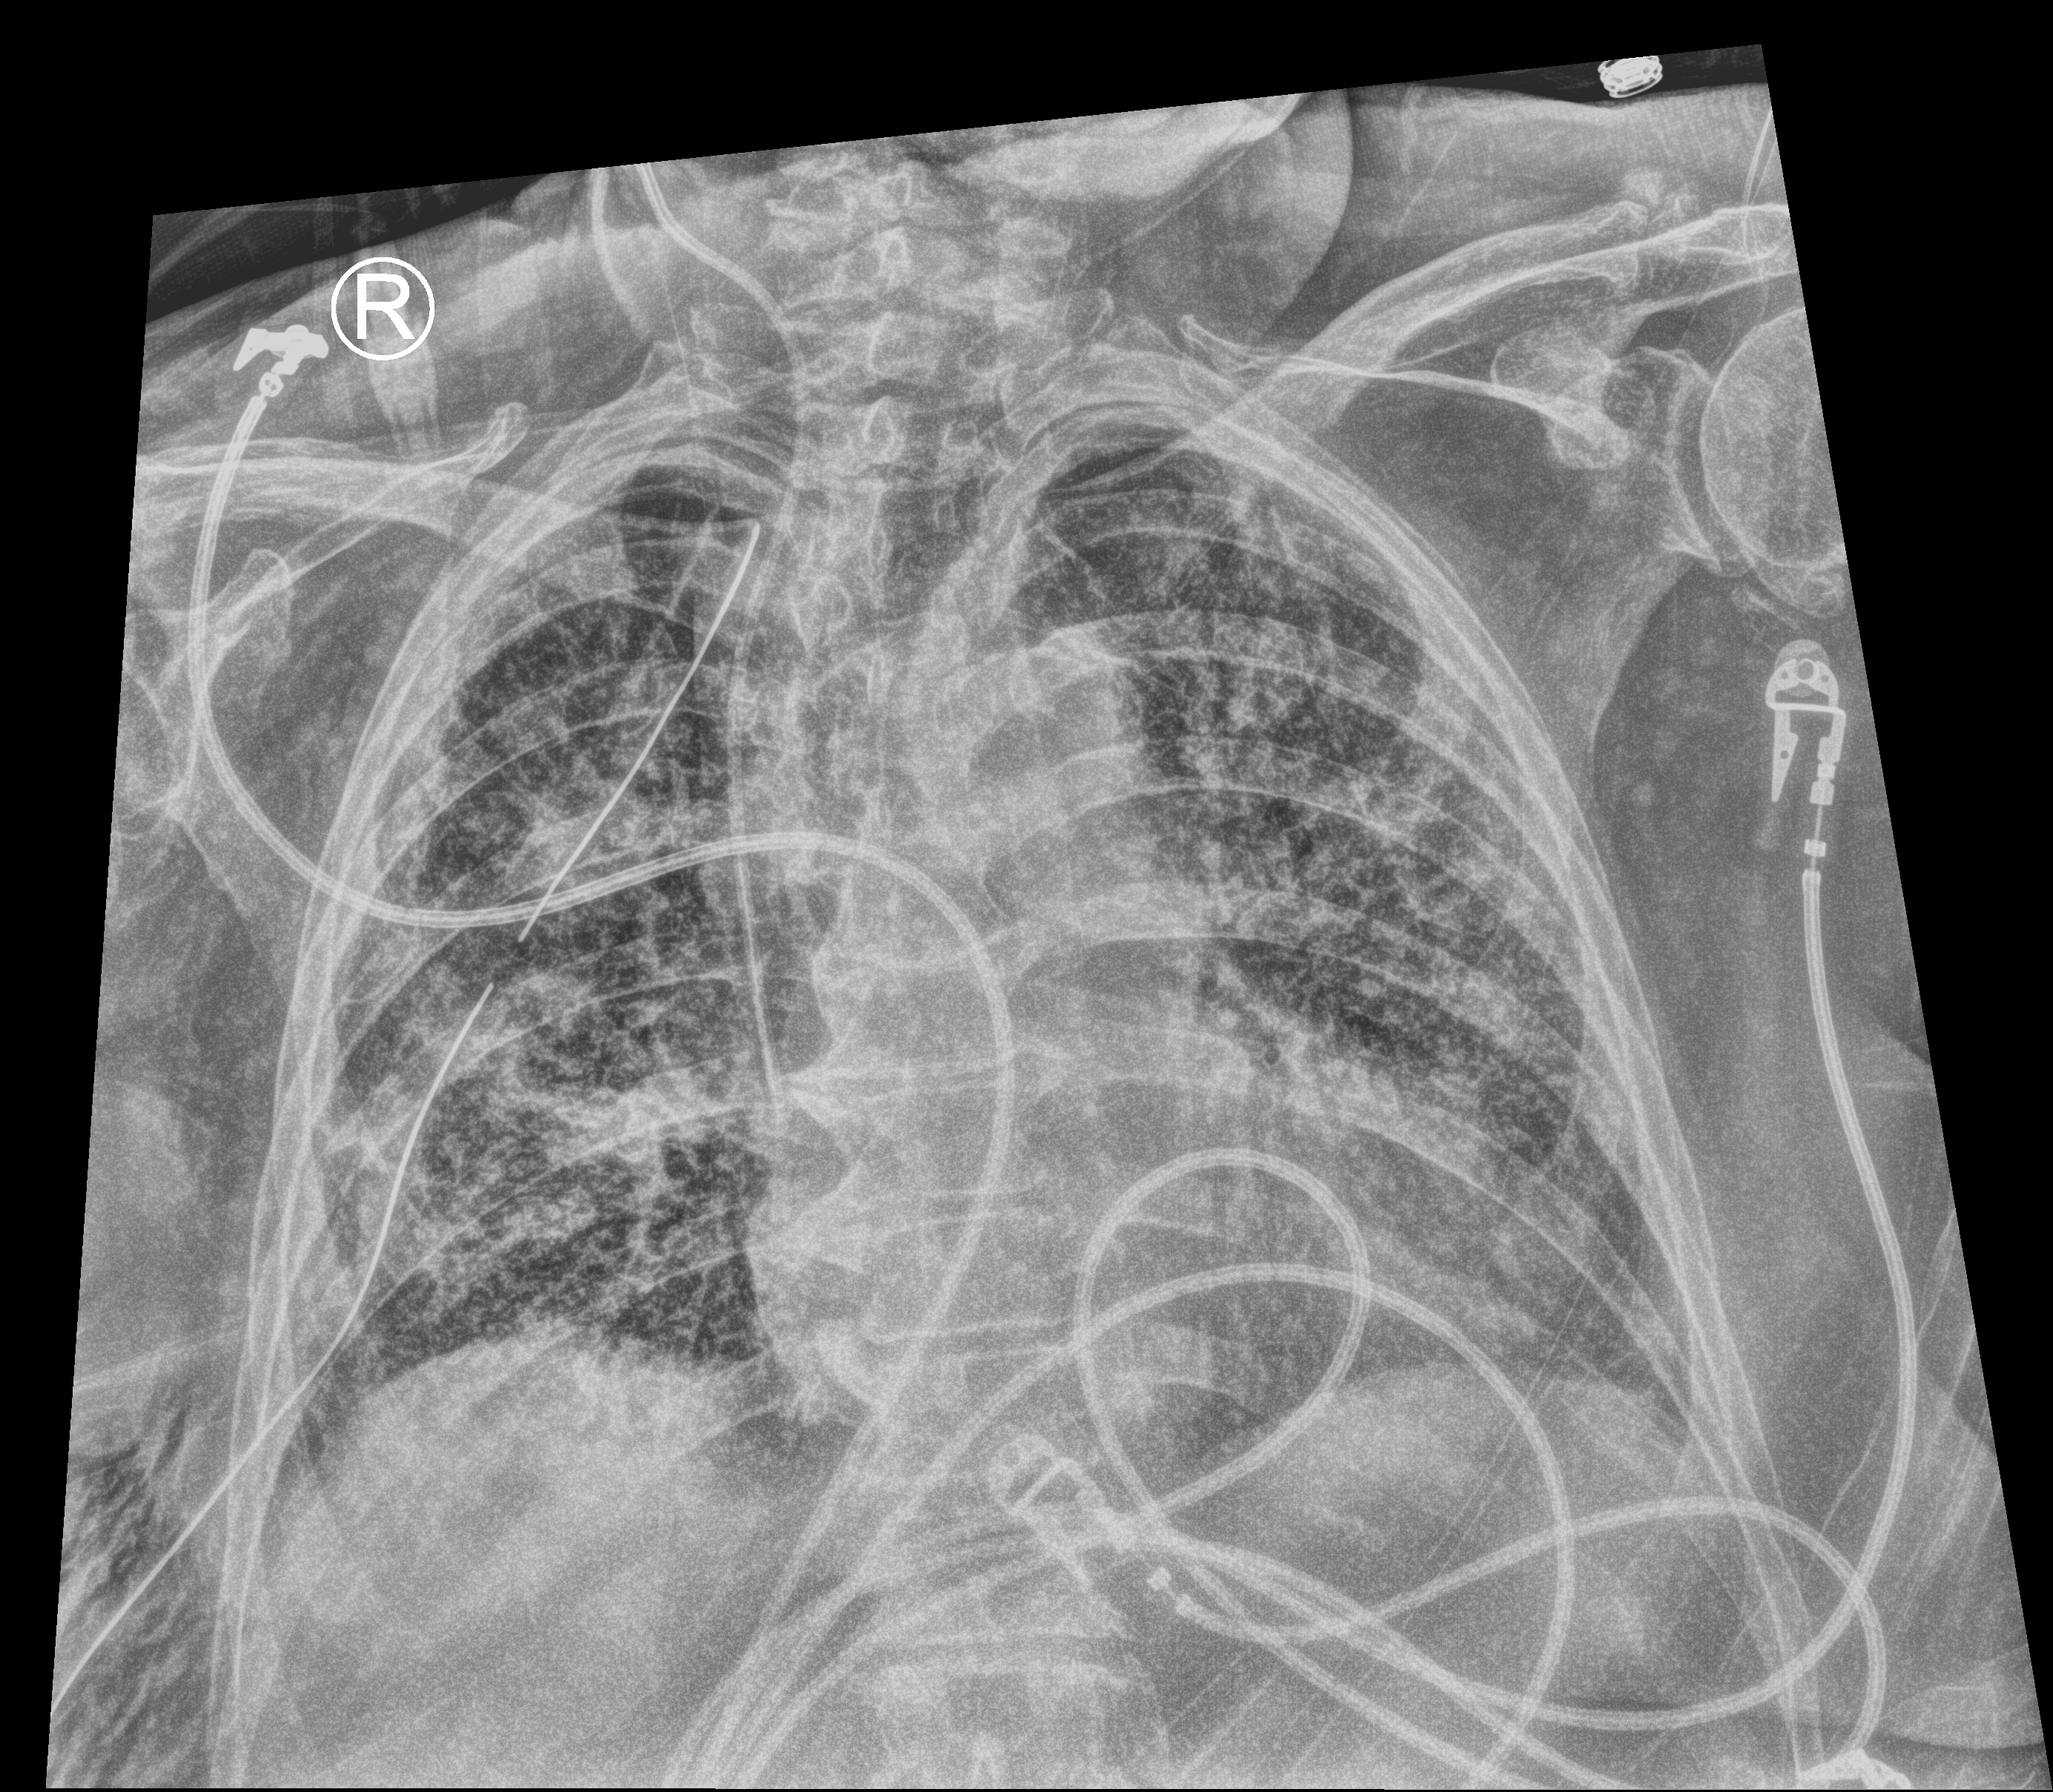
Chest X-ray (portable), anteroposterior (AP) projection. Patient hospitalised with COVID-19; female, aged 75–90 years.
From the hospital-stay record, not from the radiograph (when in the stay this image was taken is not recorded): admitted to intensive care during this hospital stay: no; mechanically ventilated during this hospital stay: yes; chronic kidney disease (admission record): no.